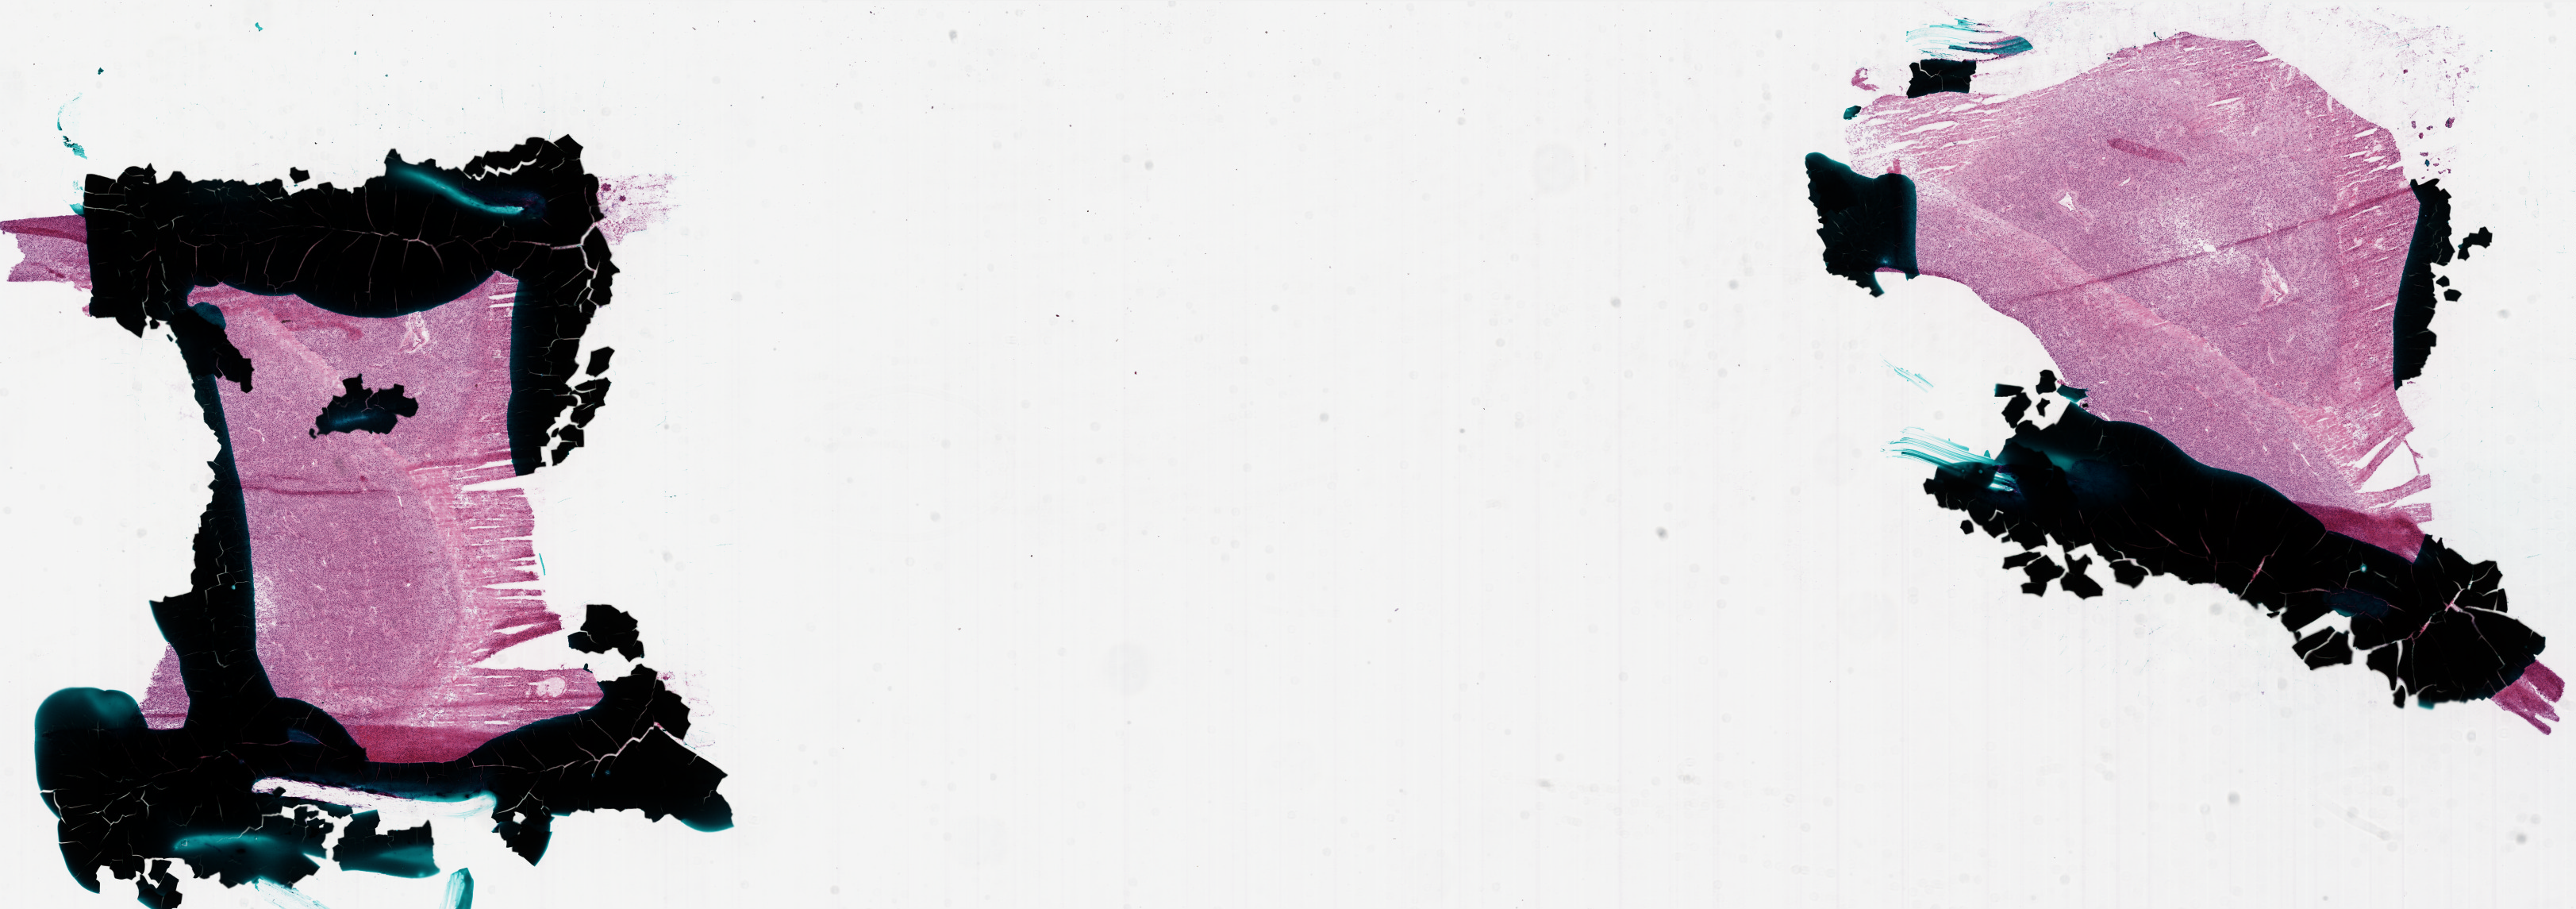
Hematoxylin and eosin (H&E) stained whole-slide image, low-resolution overview of the scanned area, about 26.0 x 9.2 mm; frozen section from the bottom of the tissue portion; sample: primary tumour, brain. Male patient; age at initial diagnosis 76 years. Pathologist review of this section (percent, as recorded): tumour cells 75%, tumour nuclei 100%, normal cells 0%, stromal cells 0%, necrosis 25%. Inflammatory infiltration, as recorded: lymphocyte infiltration 0%, monocyte infiltration 0%, neutrophil infiltration 0%.
Diagnosis: Glioblastoma.